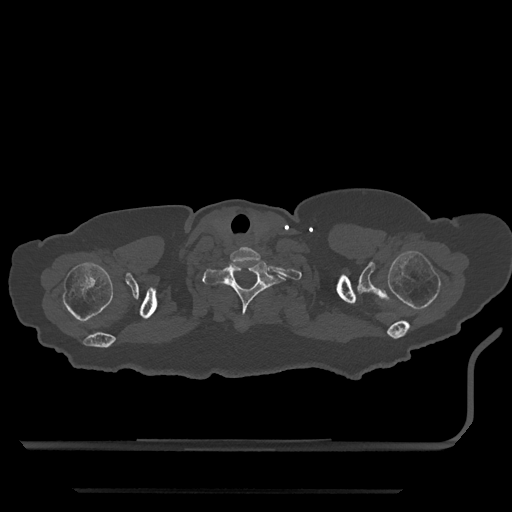
CT including the spine, one axial slice. Position 715 of 797 along the scan axis. Reconstruction kernel Br40s/3. 120 kVp. Bone window (W 1800 / L 400 HU). 0.5 mm slice thickness. 512 × 512 image matrix, field of view 440 × 440 mm. Female patient, age 51 years. Case-level facts recorded for this patient, not image findings: primary cancer: neuro; vertebrae with lytic lesions (as recorded): T8.
Structures marked on this image (semi-automatic segmentation, software-assisted and operator-edited):
- T1 vertebra: bounding box (x1, y1, x2, y2) in pixels: (203, 261, 285, 326)